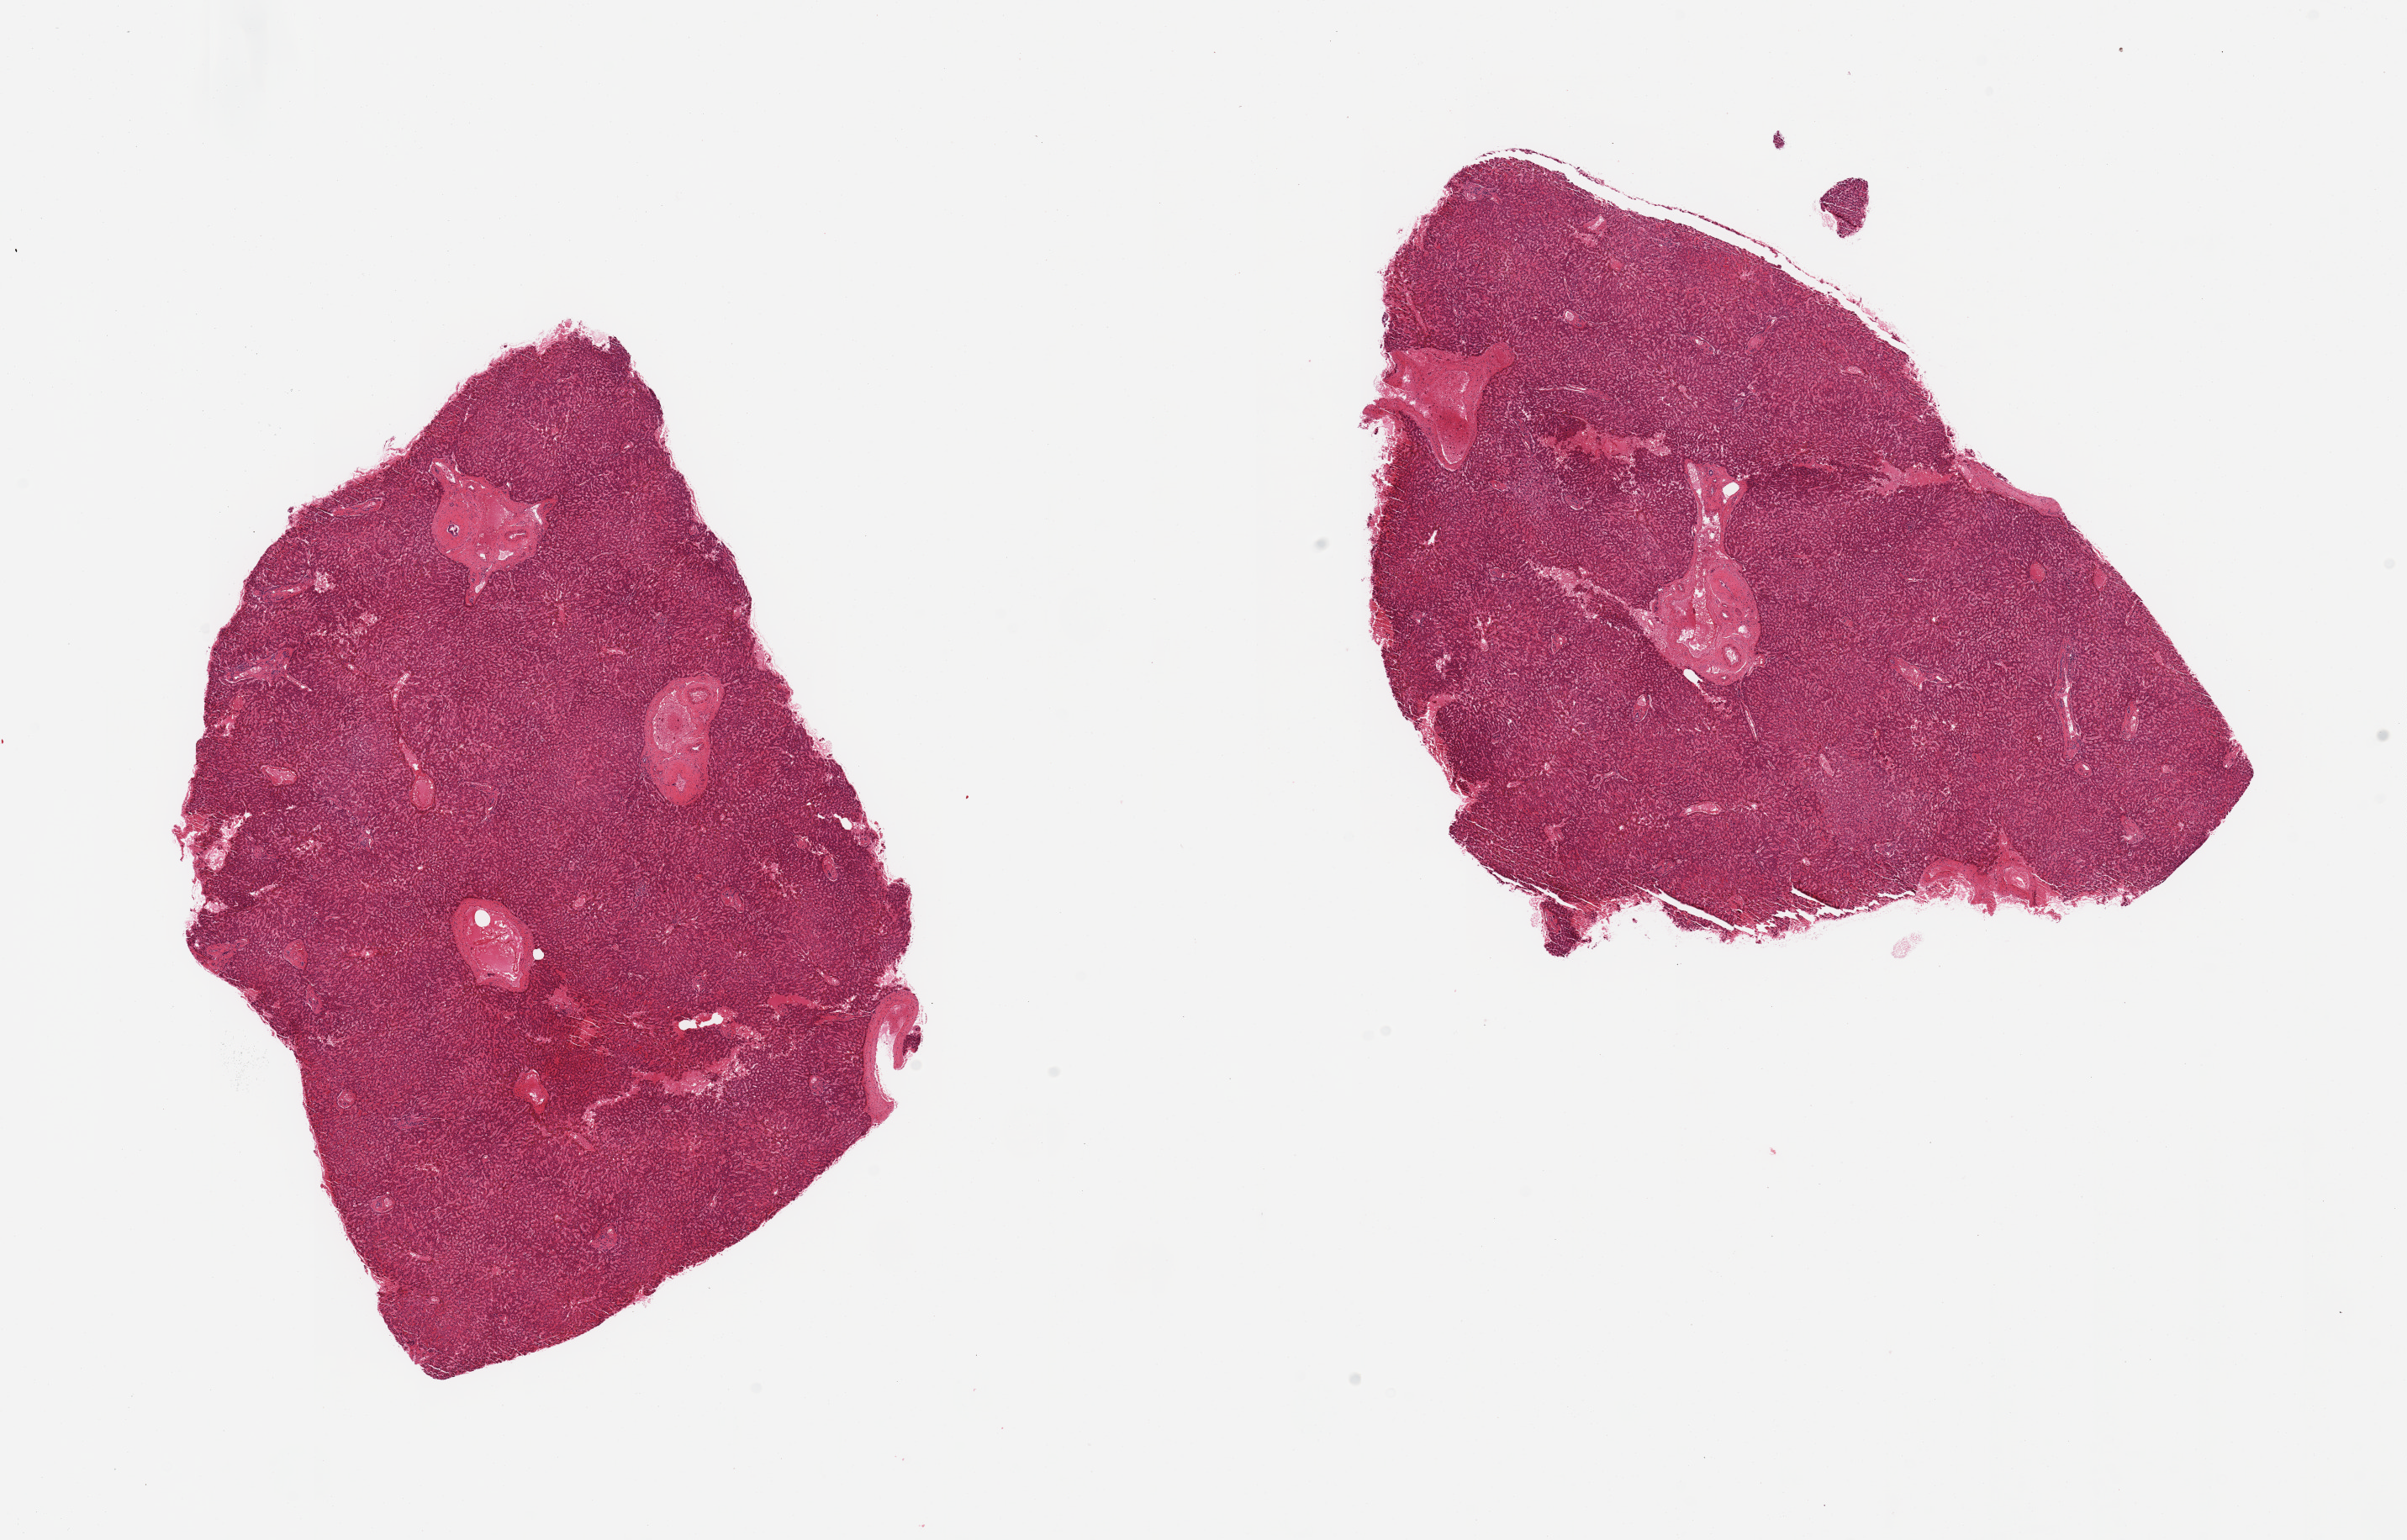
H&E whole-slide image — a low-resolution overview of the entire scanned area, about 22.6 x 14.5 mm; PAXgene-fixed, paraffin-embedded tissue; sampled site (target tissue): liver; donor tissue sample. Donor sex: female.
- reviewer comment on this tissue sample: 2 pieces, no significant steatosis/congestion